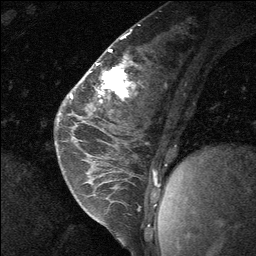
Breast MRI (dynamic contrast-enhanced), one sagittal slice. Position 27 of 64 along the scan axis. Dynamic contrast-enhanced study with each time point stored as its own series, time point 2 of 3 at this slice position (early post-contrast, ordered by acquisition time). 1.5 T. TE 4.8 ms, TR 27 ms. 2 mm slice thickness. 256 × 256 image matrix, field of view 180 × 180 mm. Patient: female, 26 years. Case-level facts recorded for this patient, not image findings: setting: breast cancer imaged before/during neoadjuvant chemotherapy; receptor status: HR-positive, HER2-negative.
Annotated regions visible in this slice (semi-automatically segmented with operator editing):
- analysis volume of interest (the breast-tissue region the enhancement analysis was run in; not a lesion): bounding box (x1, y1, x2, y2) in pixels: (86, 43, 125, 137)
- tumour enhancement mask (voxels above the 90 % enhancement threshold inside the analysis volume of interest): (102, 71, 120, 89)